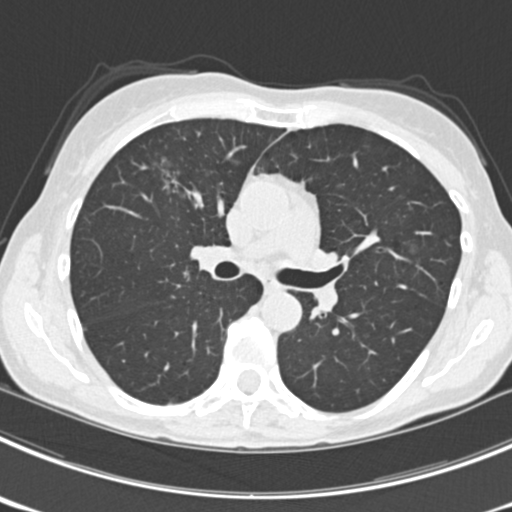
Axial slice from a low-dose chest CT screening exam; third screening round (two years after baseline); lung window (W 1500 / L -600 HU); standard (soft-tissue) reconstruction kernel (B30f); 120 kVp; slice 84 of 225 in the series. Female, age 63 years at enrolment.
Lesion marked by an expert reader, bounding box (x1, y1, x2, y2) in pixels: (146, 151, 207, 206). The screening reader recorded 9 non-calcified nodules or masses ≥4 mm on this exam (left upper lobe, right upper lobe, left upper lobe, left lower lobe, right middle lobe, left lower lobe, left lower lobe, right lower lobe, right lower lobe); which of them this box marks is not recorded.